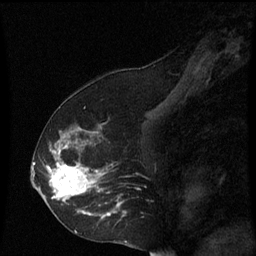
Breast MRI (dynamic contrast-enhanced), one sagittal slice. Slice 37 of 60 in the series (ordered by position). Dynamic contrast-enhanced series, image 2 of 3 at this slice position (ordered by acquisition). 1.5 T. TE 4.2 ms, TR 8.9 ms. 2 mm slice thickness. 256 × 256 image matrix, field of view 200 × 200 mm. Female patient, age 53 years. From the clinical record (not read from this slice): setting: breast cancer imaged before/during neoadjuvant chemotherapy; receptor status: HR-positive, HER2-negative.
Outlined on this slice (semi-automatic segmentation, software-assisted and operator-edited):
- analysis volume of interest (the breast-tissue region the enhancement analysis was run in; not a lesion): bounding box <38,128,127,231> (left, top, right, bottom; pixels)
- tumour enhancement mask (voxels above the 70 % enhancement threshold inside the analysis volume of interest): <46,140,121,219>